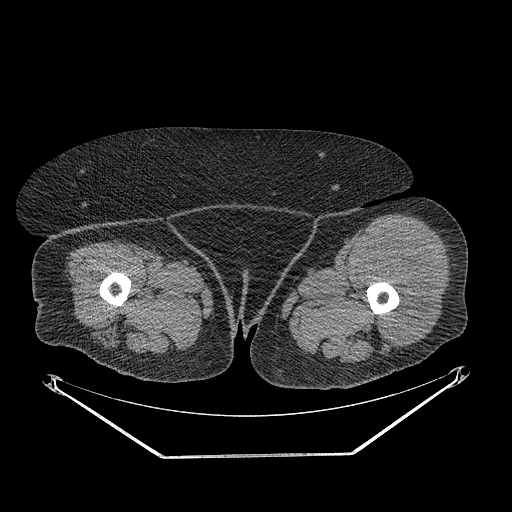
CT of an extremity soft-tissue mass (from a PET/CT study), one axial slice; position 247 of 267 along the scan axis; reconstruction kernel STANDARD; soft-tissue window (W 400 / L 40 HU); 512 × 512 image matrix. Female patient. Case-level facts recorded for this patient, not image findings: histological type: undifferentiated – high grade; grade: high; site of the primary tumour: left thigh.
Outlined on this slice (expert contour drawn on MRI and transferred to this co-registered scan by the dataset authors):
- gross tumour volume including surrounding oedema: box from (x=359, y=237) to (x=433, y=344) px
- gross tumour volume (mass): (x=361, y=242)–(x=433, y=343)